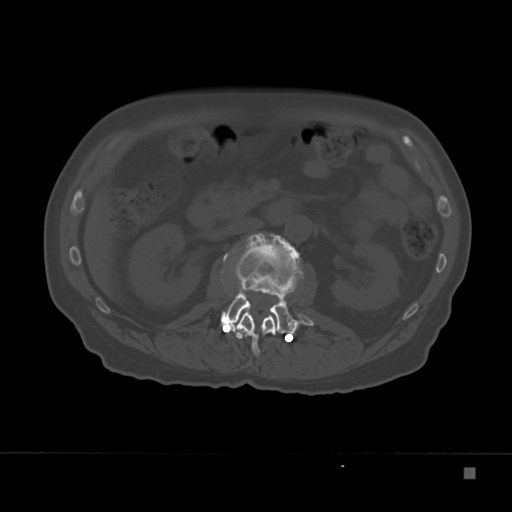
CT including the spine, one axial slice; slice 98 of 332 in the series (ordered by position); reconstruction kernel Br40s; 120 kVp; bone window (W 1800 / L 400 HU); 1.5 mm slice thickness; 512 × 512 image matrix, field of view 389 × 389 mm. Patient: male, 72 years. Case-level facts recorded for this patient, not image findings: primary cancer: skeletal.
Structures marked on this image (semi-automatically segmented with operator editing):
- L1 vertebra: bounding box <226,308,277,357> (left, top, right, bottom; pixels)
- L2 vertebra: <221,237,314,334>